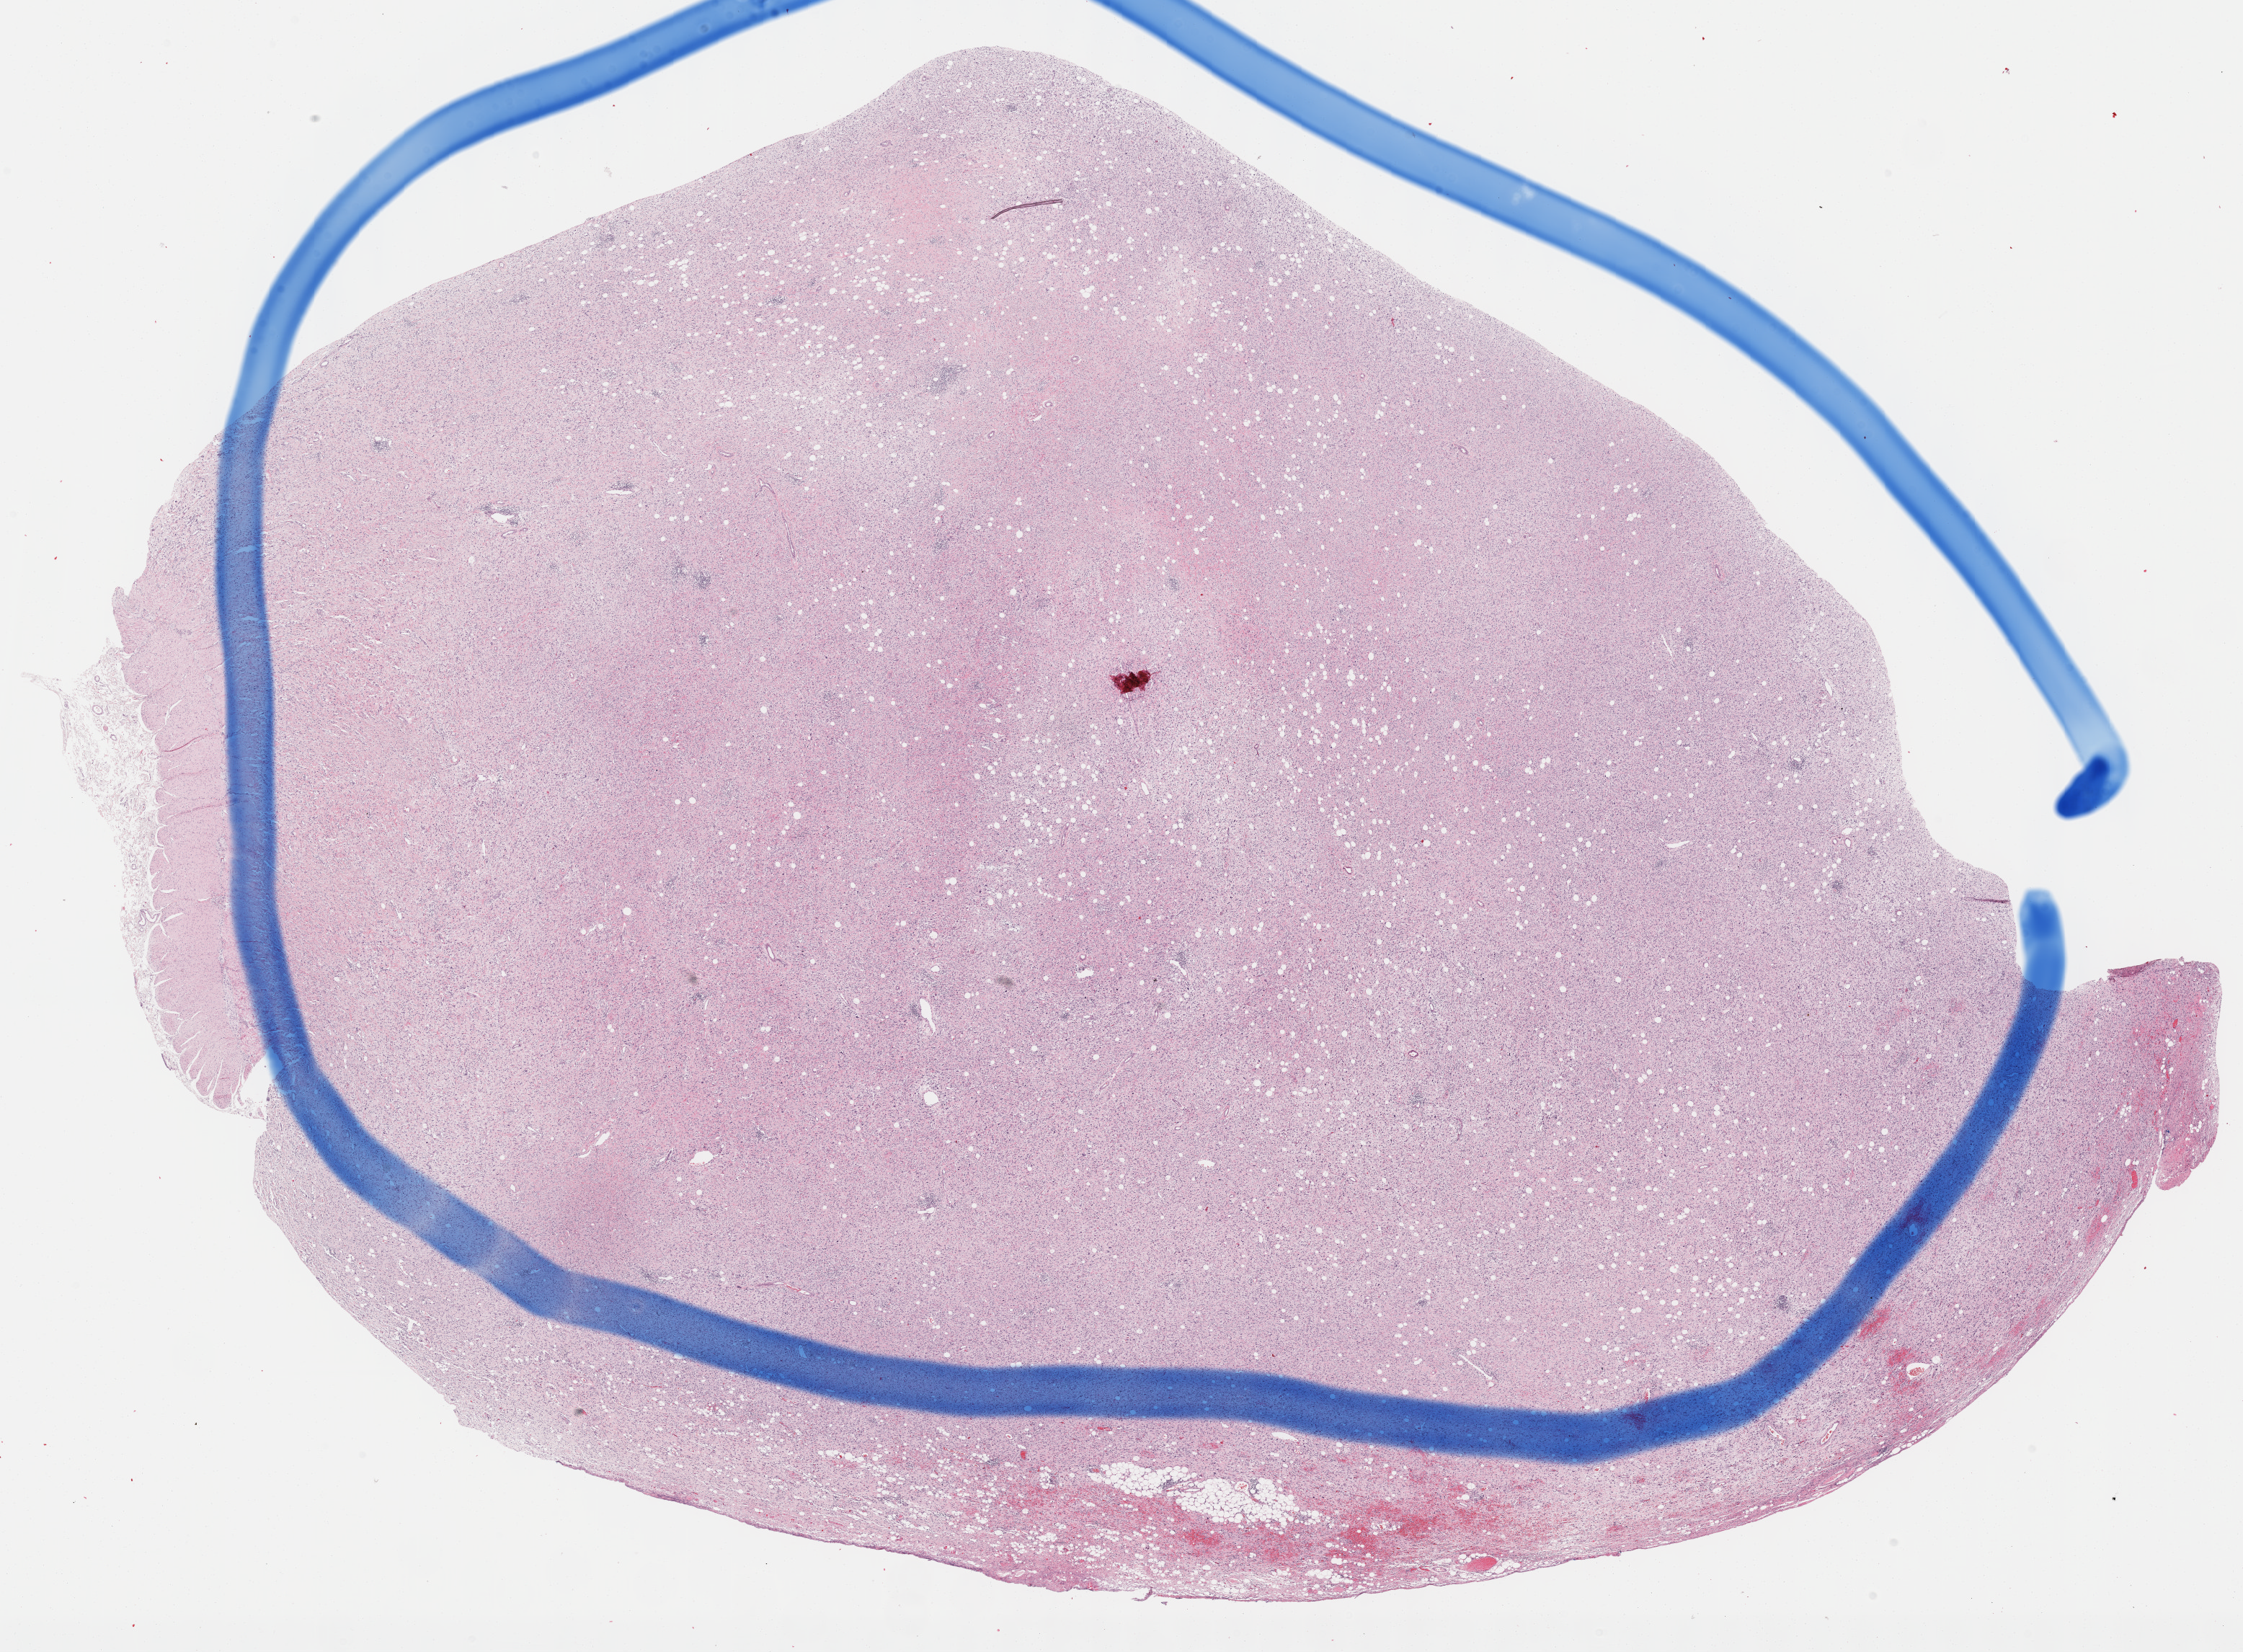
Digitized Hematoxylin and eosin (H&E) stained tissue section (whole slide), low-resolution overview of the scanned area, about 25.2 x 18.5 mm (from a 40x scan). FFPE section. Retroperitoneum and peritoneum, primary tumour sample. Female, age 57 years at initial diagnosis.
Diagnosis: Dedifferentiated liposarcoma (retroperitoneum).